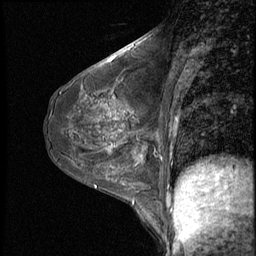
Breast MRI (dynamic contrast-enhanced), one sagittal slice; slice 28 of 50 in the series (ordered by position); 3 images stored at this slice position (order not interpretable as contrast timing); 1.5 T; TE 4.2 ms, TR 8.7 ms; 2.5 mm slice thickness; 256 × 256 image matrix, field of view 180 × 180 mm. Patient: female, 43 years. From the clinical record (not read from this slice): setting: breast cancer imaged before/during neoadjuvant chemotherapy; receptor status: HR-positive, HER2-negative.
Outlined on this slice (semi-automatically segmented with operator editing):
- analysis volume of interest (the breast-tissue region the enhancement analysis was run in; not a lesion): bounding box <122,109,159,155> (left, top, right, bottom; pixels)
- tumour enhancement mask (voxels above the 140 % enhancement threshold inside the analysis volume of interest): <122,111,127,115>